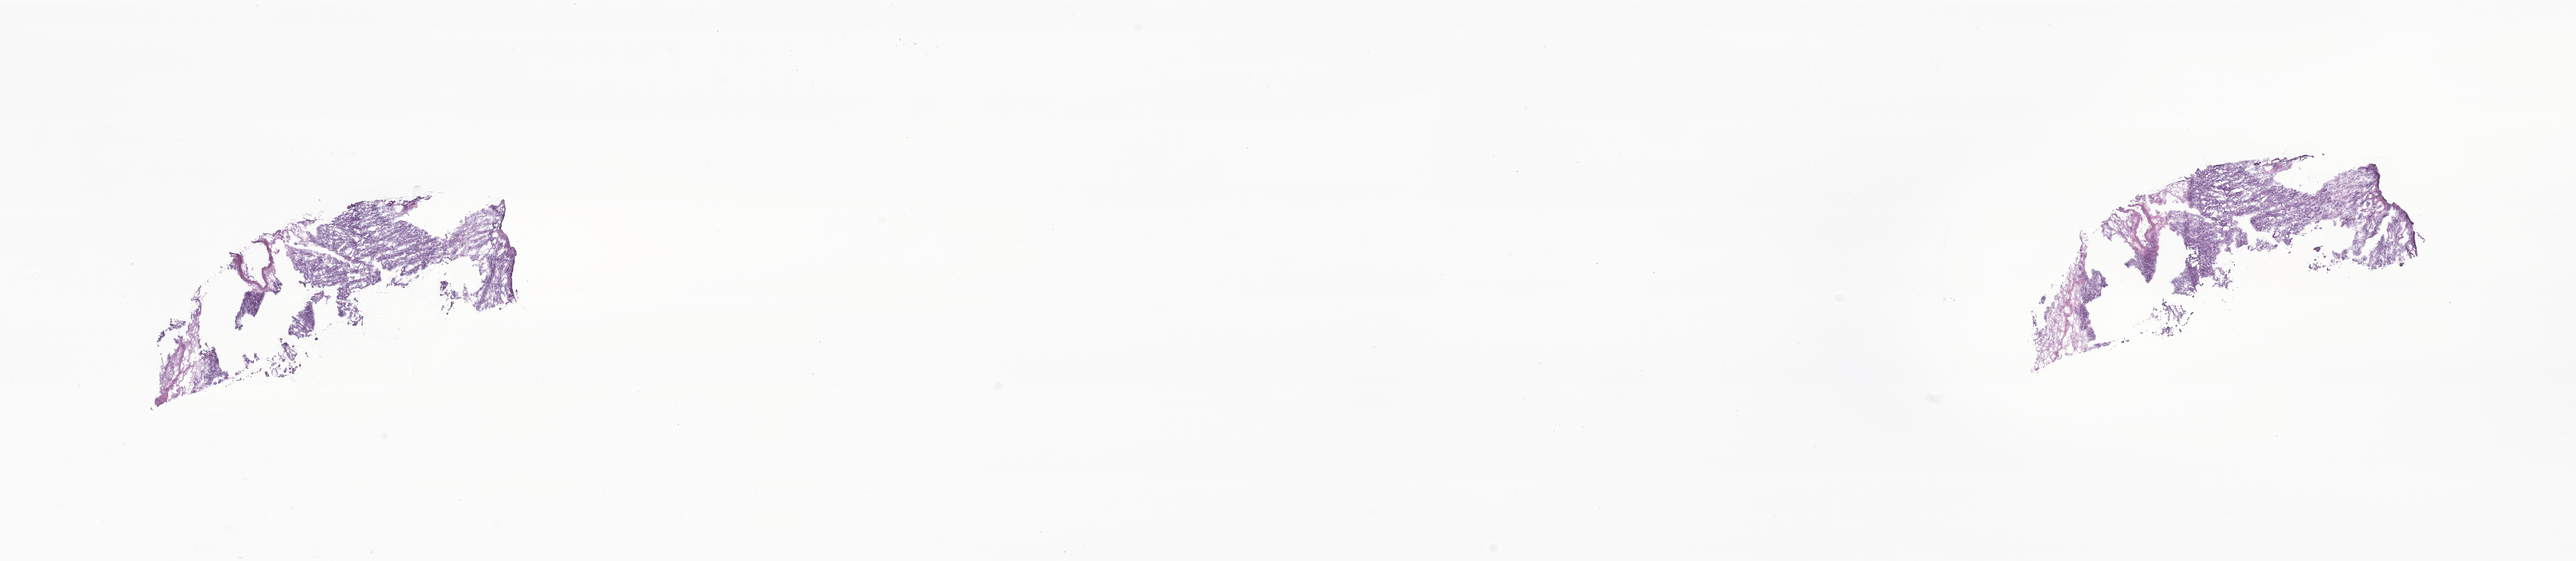
Digitized hematoxylin and eosin (H&E)-stained section of tumor tissue from the adrenal gland, a low-resolution overview of the entire scanned area, about 30.8 x 6.7 mm; frozen section. Patient: male, age 738 days (about 2.0 years).
• diagnosis (ICD-O-3 morphology term): Neuroblastoma, NOS